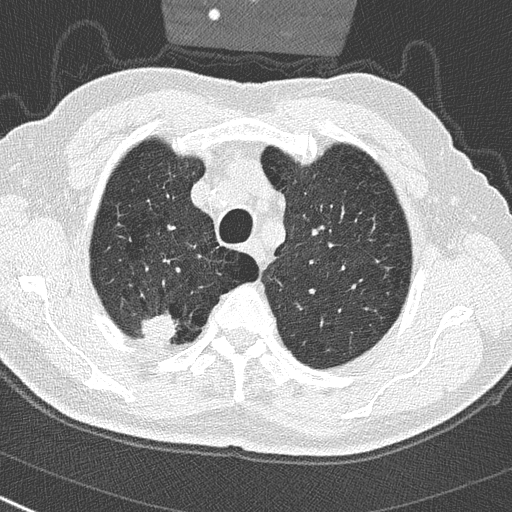
Low-dose screening chest CT, one axial slice. Slice 238 of 290 in the series (ordered by position). Reconstruction kernel B50f. 120 kVp. Lung window (W 1500 / L -600 HU). 2 mm slice thickness. 512 × 512 image matrix.
Outlined on this slice (manually delineated by an expert):
- lesion 1 (tumor, upper lobe of right lung): bounding box [x1, y1, x2, y2] px = [141, 315, 178, 343]